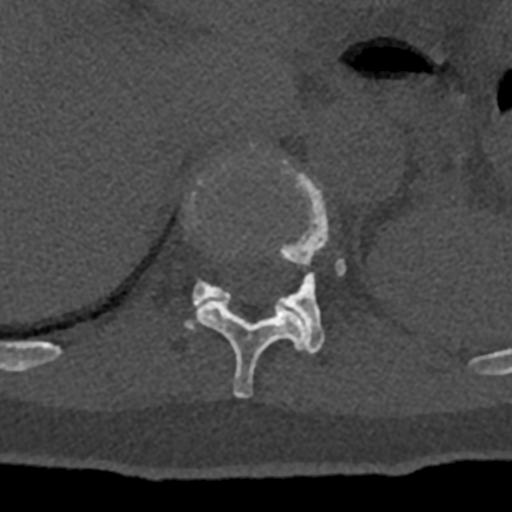
CT including the spine, one axial slice. Bone window (W 1800 / L 400 HU). 0.5 mm slice thickness. 512 × 512 image matrix, field of view 160 × 160 mm. Male patient, age 74 years. Case-level facts recorded for this patient, not image findings: primary cancer: renal; vertebrae with lytic lesions (as recorded): T10, L1, L2, L3, L4, L5.
Structures marked on this image (semi-automatically segmented with operator editing):
- T11 vertebra: box from (x=191, y=143) to (x=307, y=398) px
- T12 vertebra: (x=185, y=159)–(x=346, y=354)